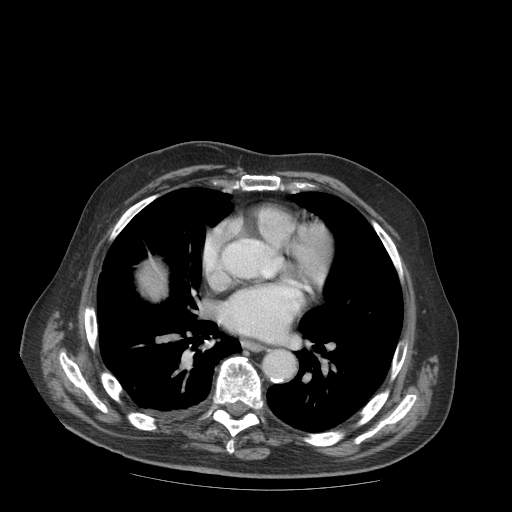
Contrast-enhanced abdominal CT (liver protocol), one axial slice. Position 98 of 99 along the scan axis. Reconstruction kernel STANDARD. 140 kVp. Soft-tissue window (W 400 / L 40 HU). 2.5 mm slice thickness. 512 × 512 image matrix, field of view 420 × 420 mm. From the clinical record (not read from this slice): diagnosis: hepatocellular carcinoma (patient treated with transarterial chemoembolisation; whether this scan precedes or follows treatment is not stated here); TNM stage (as recorded): Stage-IIIB; Child-Pugh class: A.
Annotated regions visible in this slice (semi-automatic segmentation, software-assisted and operator-edited):
- liver parenchyma outside the tumour (the mass and vessels are separate outlines, so this box may not span the whole liver): bounding box (x1, y1, x2, y2) in pixels: (139, 259, 166, 299)